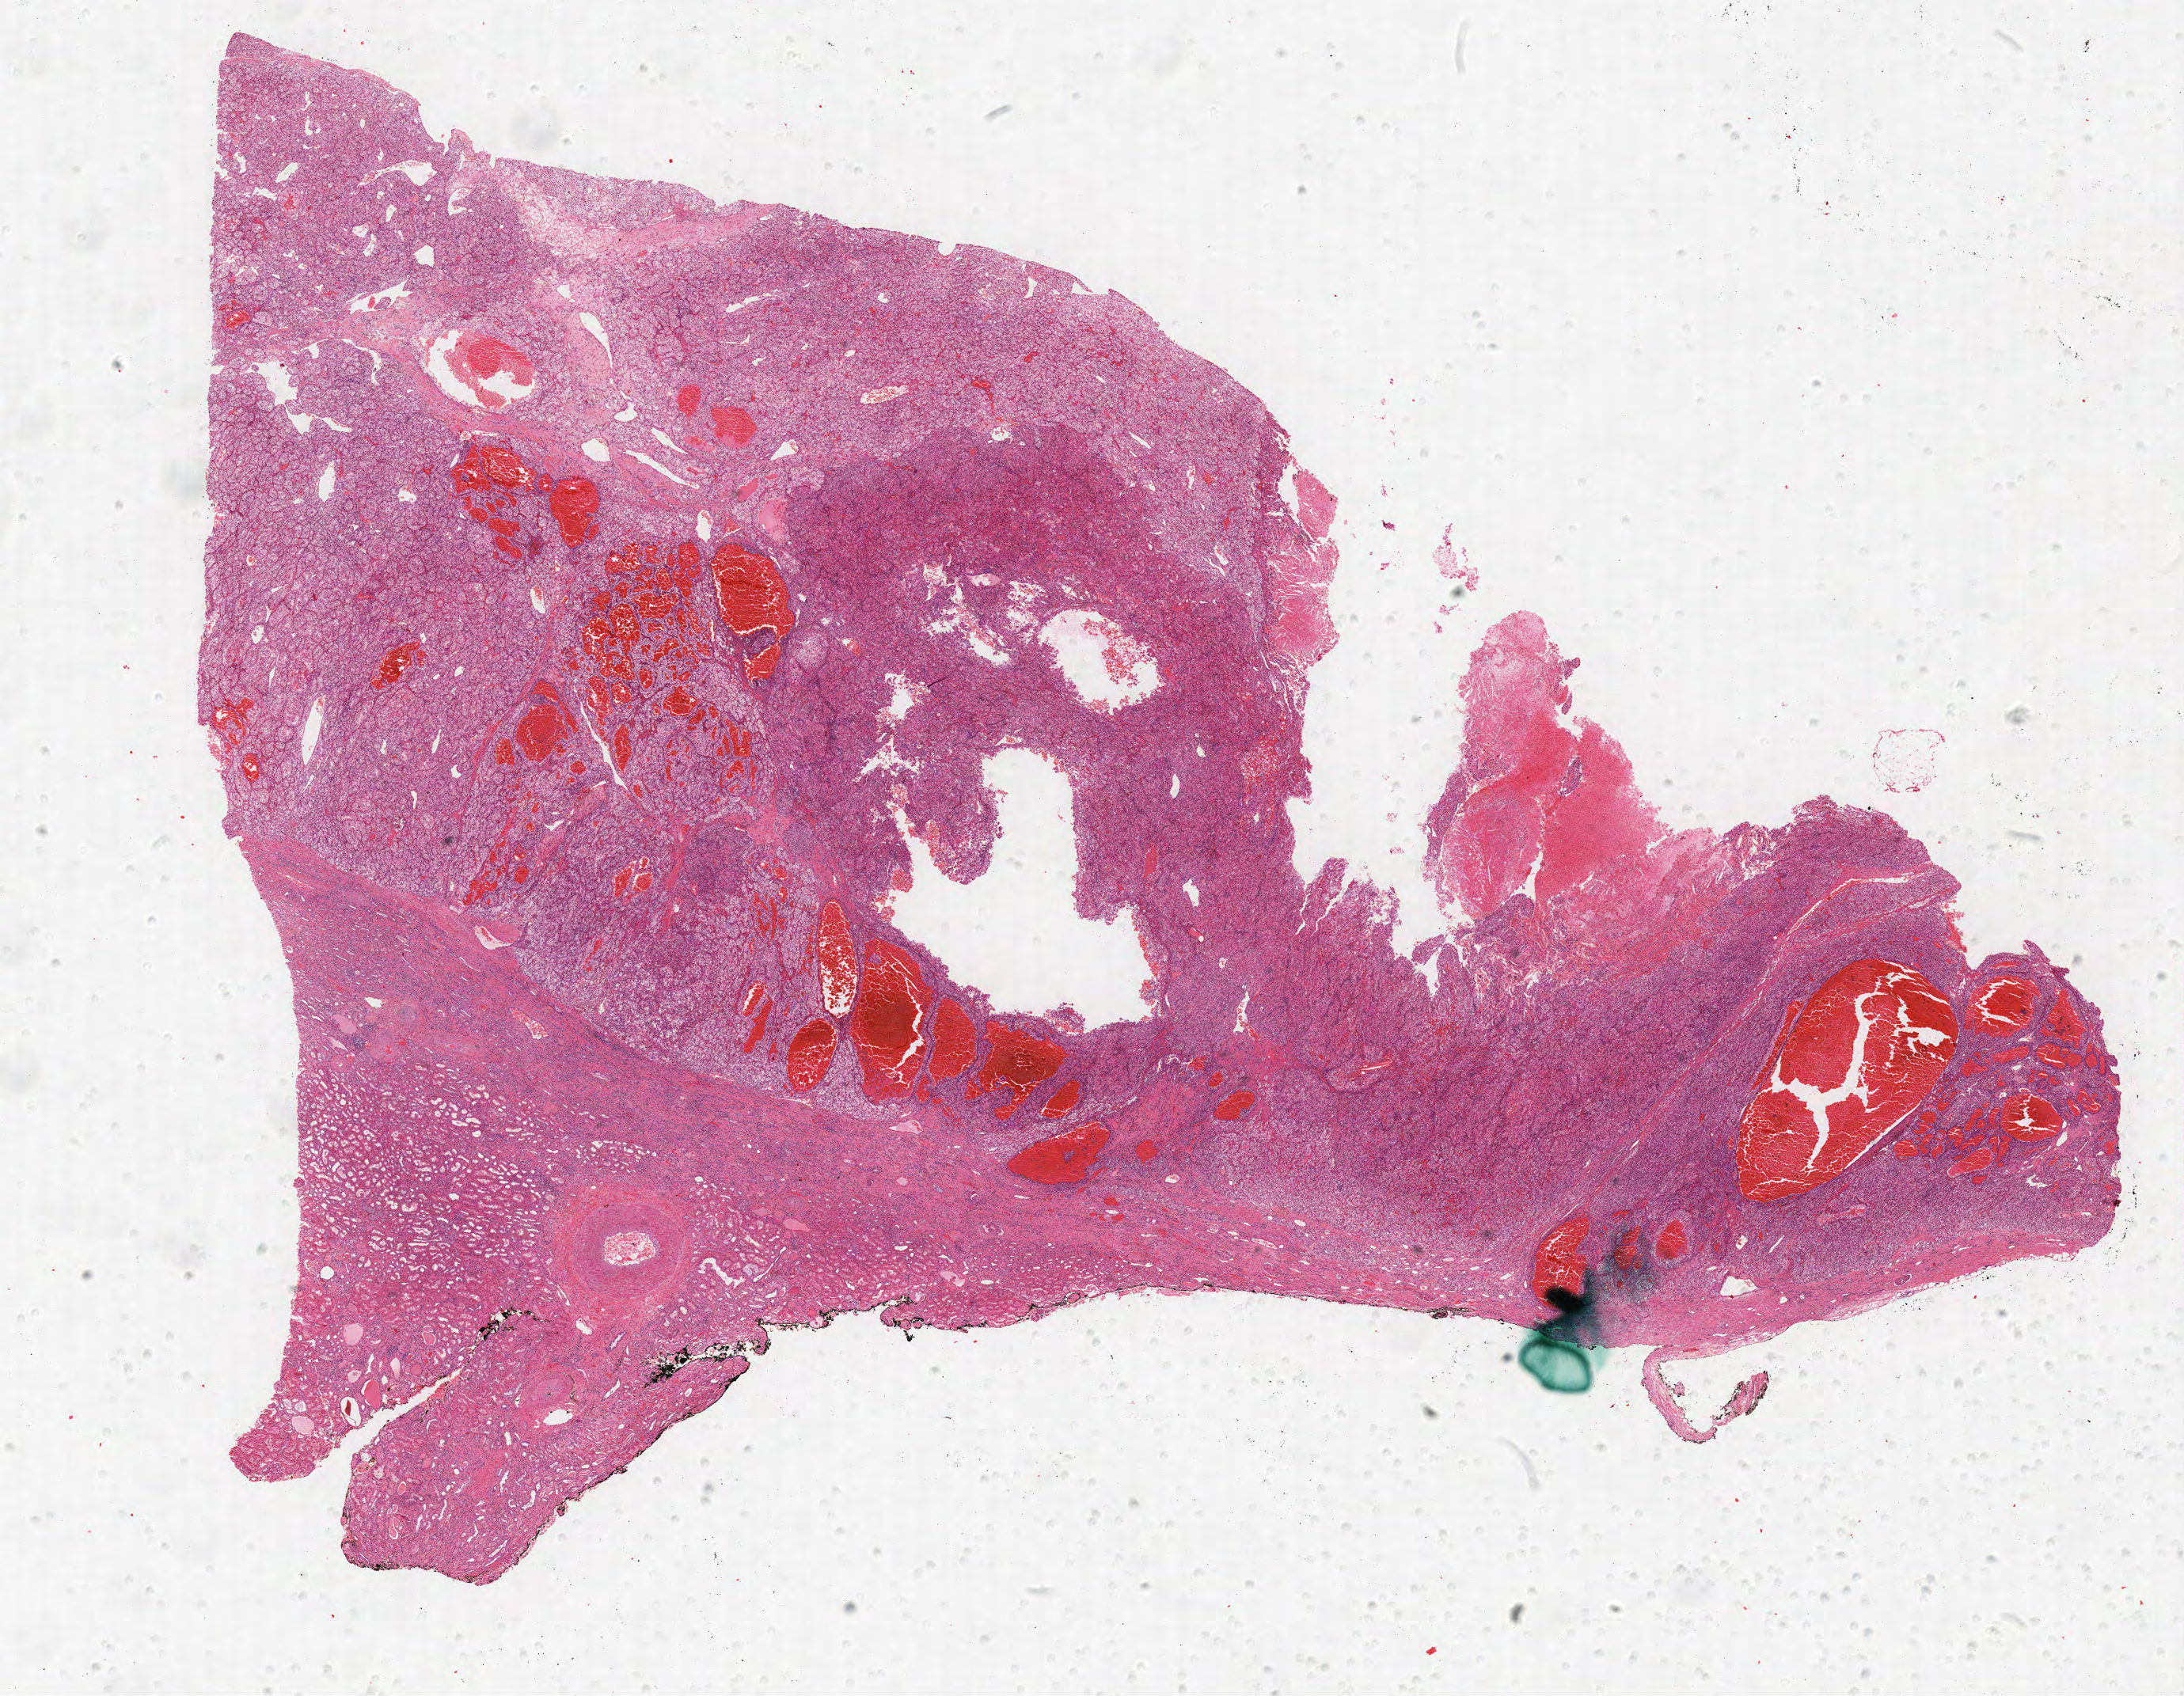
Digitized Hematoxylin and eosin (H&E) stained tissue section (whole slide) — a low-resolution overview of the entire scanned area, about 22.1 x 17.1 mm, formalin-fixed paraffin-embedded (FFPE) diagnostic section, kidney, primary tumour sample. Male patient; age at initial diagnosis 52 years. Histologic grade: G2 (moderately differentiated).
Histologic diagnosis: Clear cell adenocarcinoma, NOS. AJCC pathologic stage: I. Laterality: left.